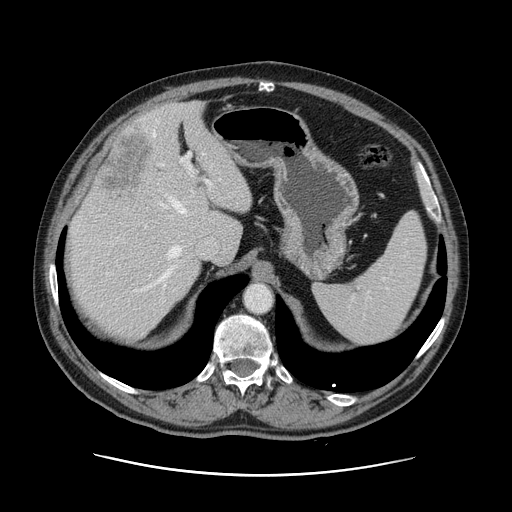
Contrast-enhanced abdominal CT, one axial slice; position 92 of 141 along the scan axis; soft-tissue window (W 400 / L 40 HU); 2.5 mm slice thickness; 512 × 512 image matrix. Male patient, age 72 years. Case-level facts recorded for this patient, not image findings: diagnosis: colorectal cancer liver metastases, imaged before liver resection; multiple liver metastases: yes; largest metastasis: 5.4 cm.
Structures marked on this image (expert manual segmentation):
- hepatic veins: bounding box (x1, y1, x2, y2) in pixels: (134, 153, 204, 291)
- liver: (68, 104, 251, 337)
- planned liver remnant (the part of the liver to remain after resection): (68, 103, 251, 336)
- portal vein (with intrahepatic branches): (144, 152, 212, 228)
- liver metastasis: (100, 128, 154, 202)